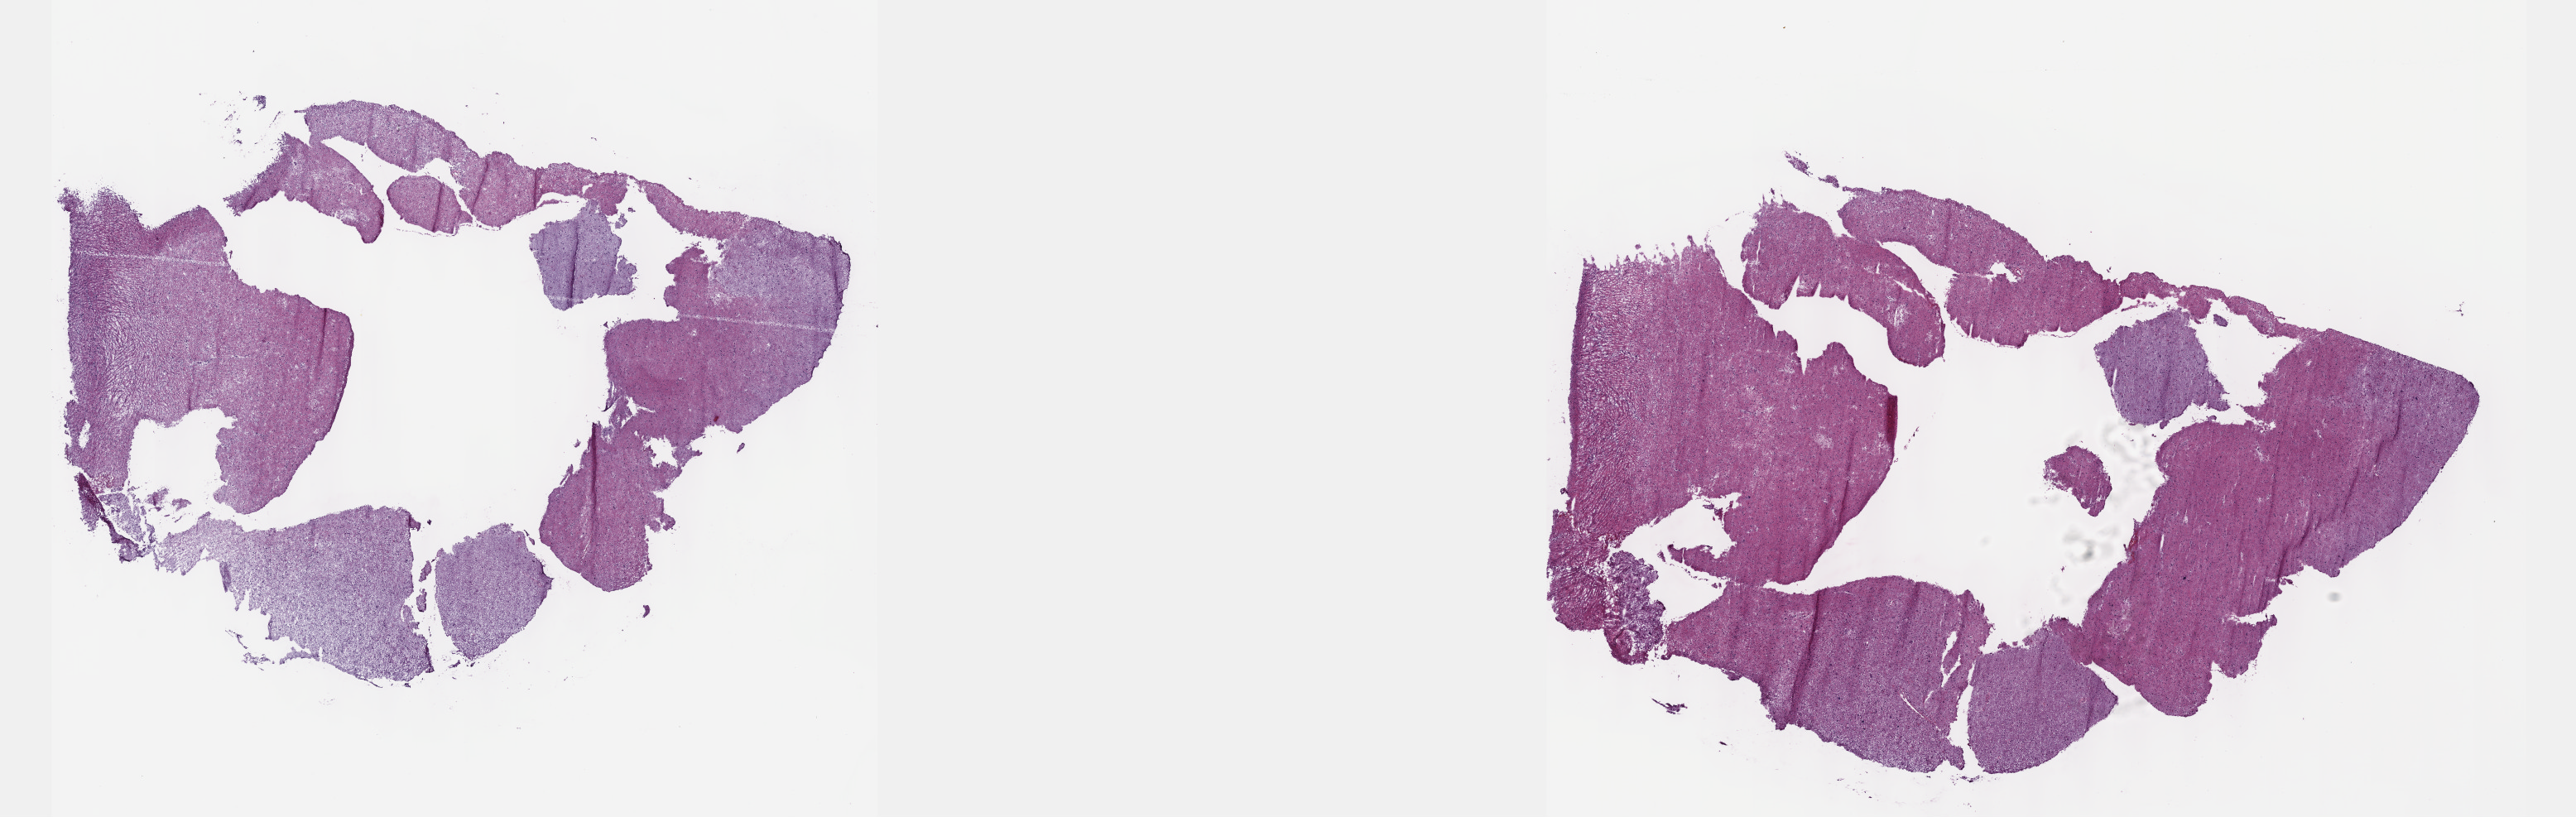
Hematoxylin and eosin (H&E) stained whole-slide image, whole scanned area (about 25.1 x 8.0 mm) shown as a low-resolution overview. Frozen section. Sample: primary tumour, brain. Female, age 61 years at initial diagnosis. Histologic grade: G3 (poorly differentiated). Pathologist review of this section (percent, as recorded): tumour cells 30%, tumour nuclei 80%, normal cells 10%, stromal cells 60%, necrosis 0%. Inflammatory infiltration, as recorded: lymphocyte infiltration 0%, monocyte infiltration 0%, neutrophil infiltration 0%.
Histologic diagnosis: Astrocytoma, anaplastic (cerebrum).